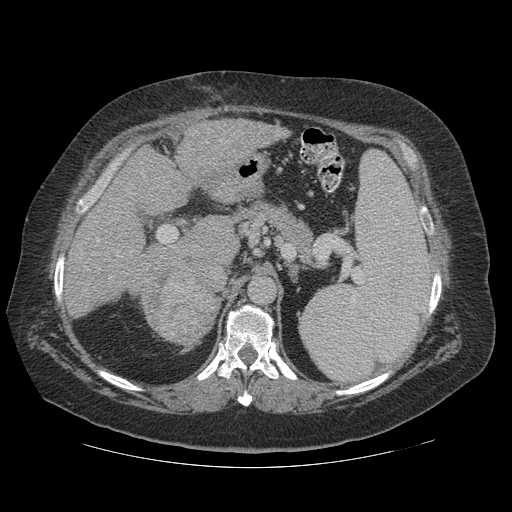
Contrast-enhanced abdominal CT (liver protocol), one axial slice. Slice 71 of 121 in the series (ordered by position). Reconstruction kernel STANDARD. 140 kVp. Soft-tissue window (W 400 / L 40 HU). 2.5 mm slice thickness. 512 × 512 image matrix, field of view 420 × 420 mm. Case-level facts recorded for this patient, not image findings: diagnosis: hepatocellular carcinoma (patient treated with transarterial chemoembolisation; whether this scan precedes or follows treatment is not stated here); TNM stage (as recorded): Stage-IIIA; Child-Pugh class: A; tumour differentiation: well differentiated.
Structures marked on this image (semi-automatic segmentation, software-assisted and operator-edited):
- liver parenchyma outside the tumour (the mass and vessels are separate outlines, so this box may not span the whole liver): bounding box [x1, y1, x2, y2] px = [64, 120, 289, 338]
- mass: [138, 249, 217, 345]
- liver vessels: [91, 140, 221, 278]